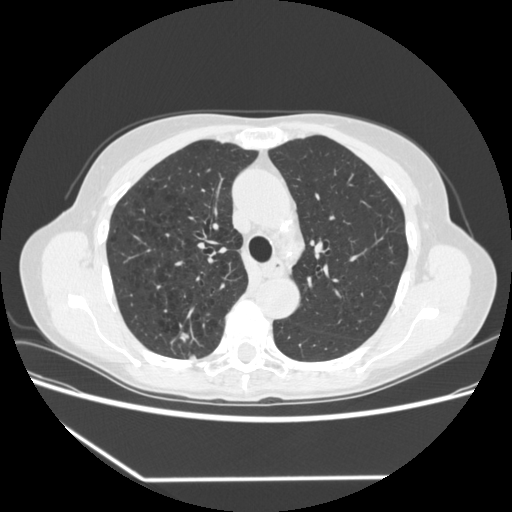
Axial slice from a low-dose chest CT screening exam; baseline screening round; lung window (W 1500 / L -600 HU); 1.25 mm slice thickness; standard (soft-tissue) reconstruction kernel (STANDARD); slice 233 of 323 in the series; 512 × 512 image matrix. Female participant, aged 67 years at enrolment. Current smoker at enrolment.
- Expert reader's lesion annotation, bounding box (x1, y1, x2, y2) in pixels: (159, 324, 203, 365).
- The screening reader recorded 2 non-calcified nodules or masses ≥4 mm on this exam (right upper lobe, right lower lobe); which of them this box marks is not recorded.
- Participant outcome: lung cancer diagnosed 29 days after this screen — adenocarcinoma, NOS, right upper lobe, moderately differentiated (G2), stage IA (AJCC 6th edition), 24 mm at pathology.